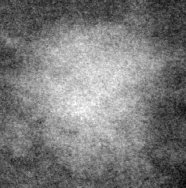
Cropped region of a digitized screen-film mammogram centred on a radiologist-marked abnormality; left breast; CC view; BI-RADS breast density category 1 (scale 1–4).
- Finding: mass, shape lobulated, margins ill defined; BI-RADS assessment category 4; pathology result (as recorded, not read from the image): malignant.